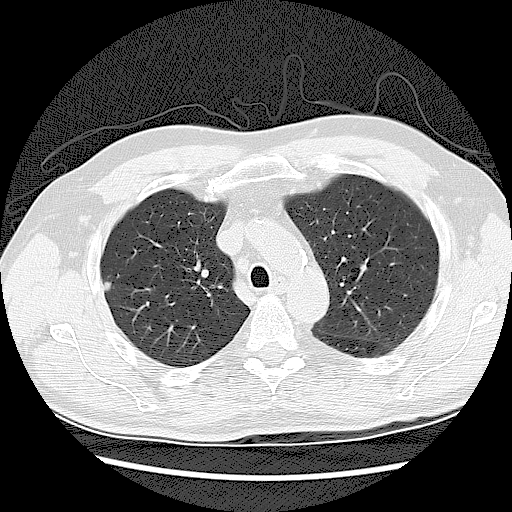
Low-dose screening chest CT, one axial slice; slice 87 of 120 in the series (ordered by position); reconstruction kernel LUNG; lung window (W 1500 / L -600 HU); 512 × 512 image matrix, field of view 360 × 360 mm.
Outlined on this slice (expert manual segmentation):
- lesion 1 (tumor, upper lobe of right lung): bounding box [x1, y1, x2, y2] px = [104, 281, 114, 291]